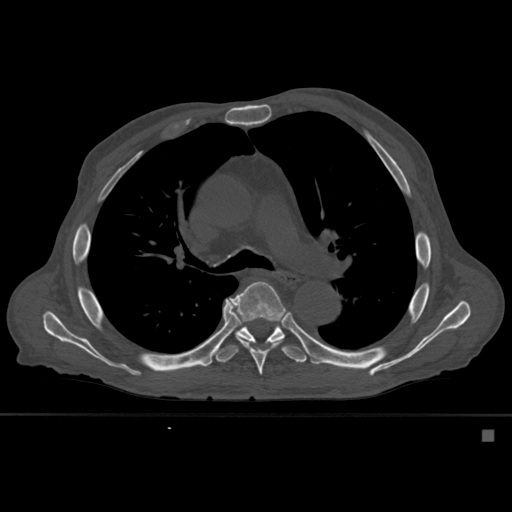
CT including the spine, one axial slice; position 378 of 527 along the scan axis; bone window (W 1800 / L 400 HU); 1.5 mm slice thickness; 512 × 512 image matrix, field of view 373 × 373 mm. Patient: male, 78 years. From the clinical record (not read from this slice): primary cancer: prostate.
Outlined on this slice (semi-automatic segmentation, software-assisted and operator-edited):
- T6 vertebra: bounding box <225,281,288,375> (left, top, right, bottom; pixels)
- T7 vertebra: <213,320,307,363>